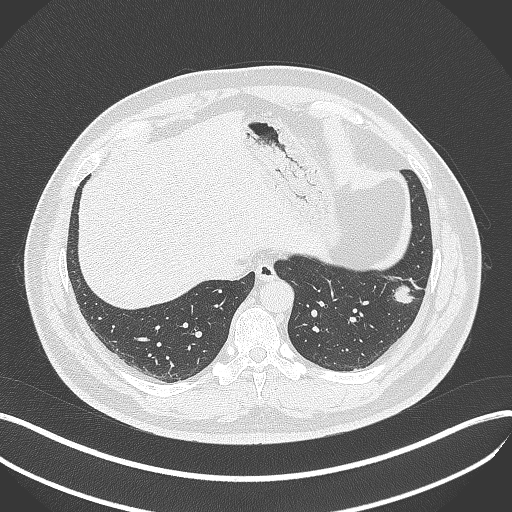
Chest CT, one axial slice. Position 110 of 429 along the scan axis. Reconstruction kernel B70f. Lung window (W 1500 / L -600 HU). 512 × 512 image matrix, field of view 400 × 400 mm. Male patient, age 39 years. From the clinical record (not read from this slice): clinical TNM (as recorded): T2a N0 M0.
Annotated regions visible in this slice (rectangle marked by the reading radiologist):
- lung tumour (recorded histology: adenocarcinoma): bounding box <387,280,415,308> (left, top, right, bottom; pixels)